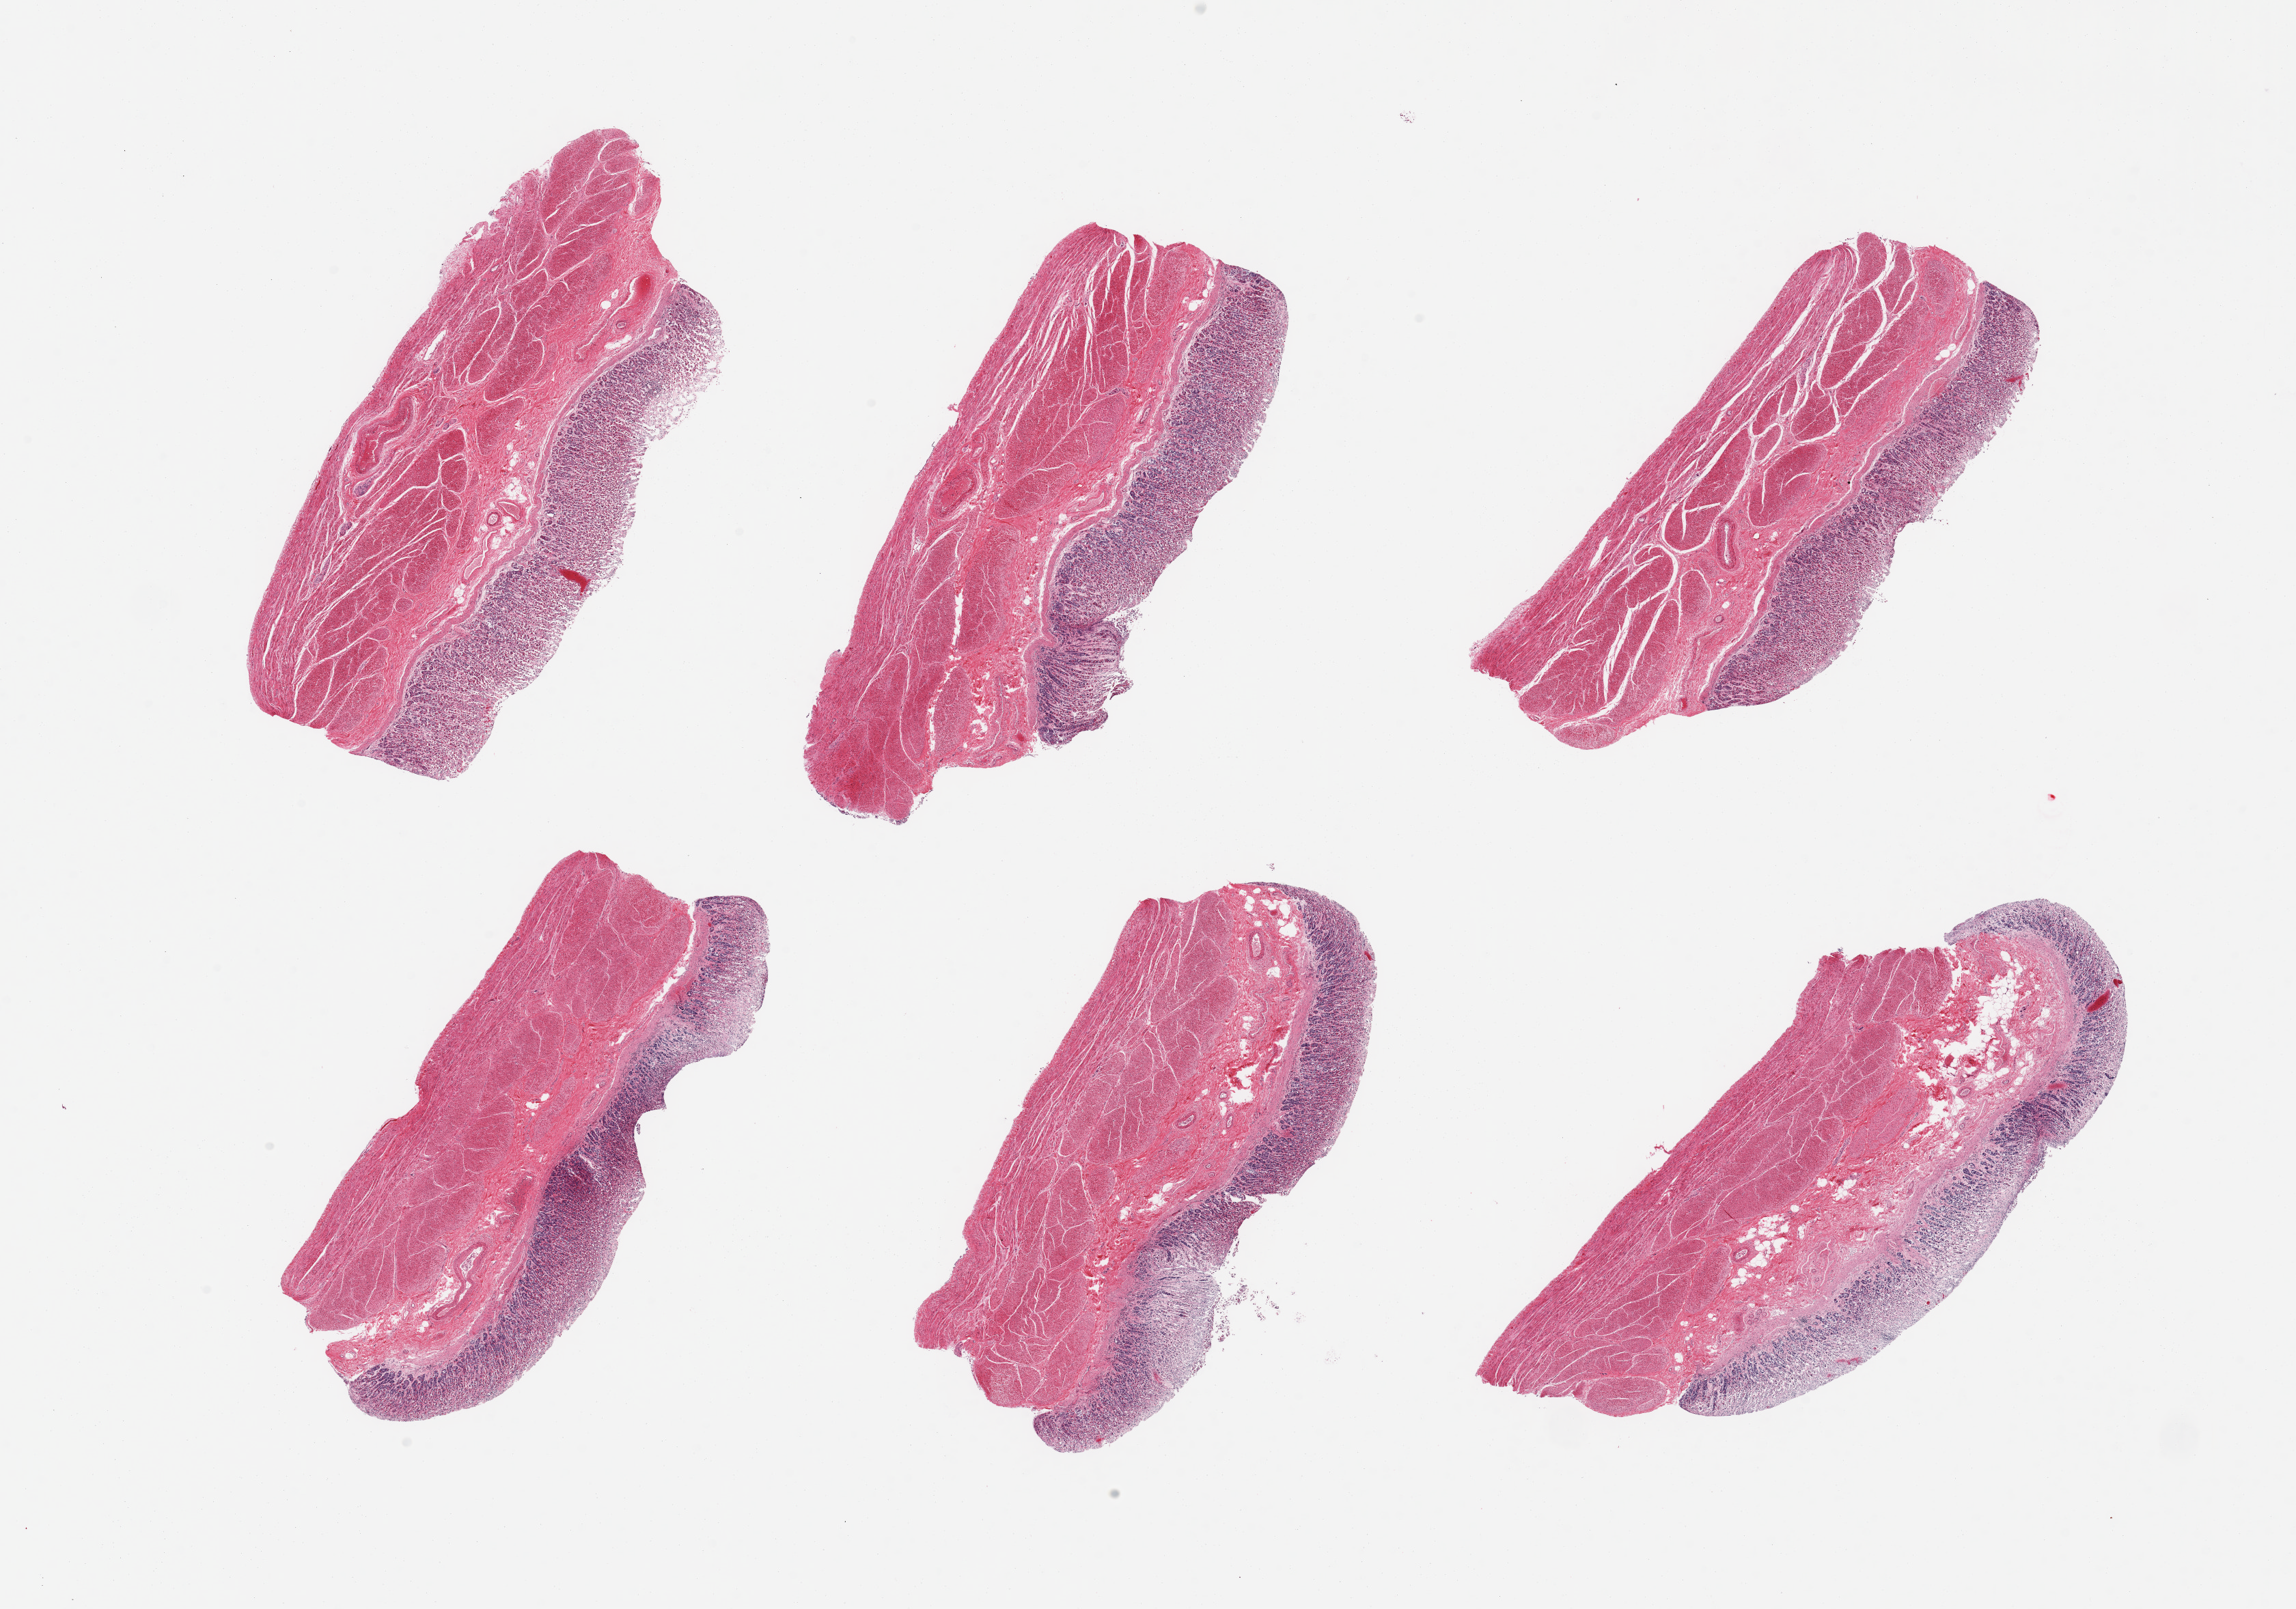
Haematoxylin and eosin whole-slide image, whole scanned area (about 26.6 x 18.6 mm) shown as a low-resolution overview. PAXgene-fixed paraffin-embedded (PFPE) section. Sampled site (target tissue): stomach. Donor tissue sample. Donor: male.
Reviewer comment on this tissue sample: 6 pieces; mucosa varies from moderate to severe autolysis; muscle varies from slight to moderate autolysis.